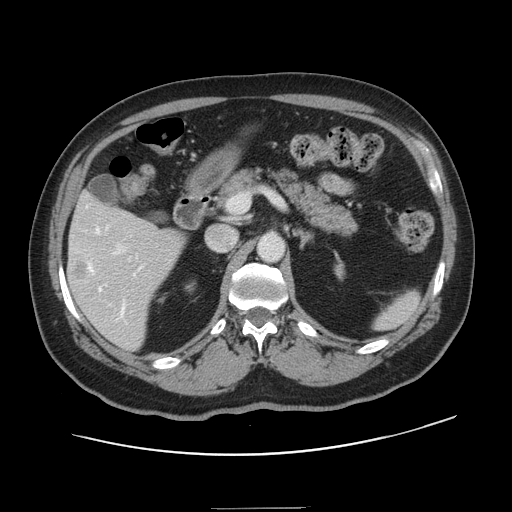
Contrast-enhanced abdominal CT, one axial slice. Slice 76 of 143 in the series (ordered by position). 120 kVp. Soft-tissue window (W 400 / L 40 HU). 2.5 mm slice thickness. 512 × 512 image matrix, field of view 402 × 402 mm. Male patient, age 62 years. From the clinical record (not read from this slice): diagnosis: colorectal cancer liver metastases, imaged before liver resection; multiple liver metastases: yes; largest metastasis: 2.7 cm; disease in both lobes: no.
Annotated regions visible in this slice (expert manual segmentation):
- hepatic veins: bounding box <86,206,141,316> (left, top, right, bottom; pixels)
- liver: <68,196,182,349>
- planned liver remnant (the part of the liver to remain after resection): <74,196,134,226>
- portal vein (with intrahepatic branches): <109,245,125,305>
- liver metastasis: <75,264,87,280>